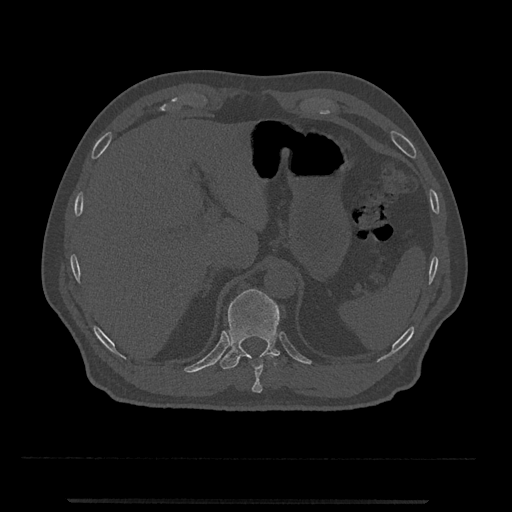
CT including the spine, one axial slice. Position 482 of 797 along the scan axis. Reconstruction kernel Br40s/3. 120 kVp. Bone window (W 1800 / L 400 HU). 0.5 mm slice thickness. 512 × 512 image matrix. Patient: male, 63 years. From the clinical record (not read from this slice): primary cancer: prostate.
Annotated regions visible in this slice (semi-automatic segmentation, software-assisted and operator-edited):
- T10 vertebra: bounding box <252,354,275,393> (left, top, right, bottom; pixels)
- T11 vertebra: <219,289,281,369>